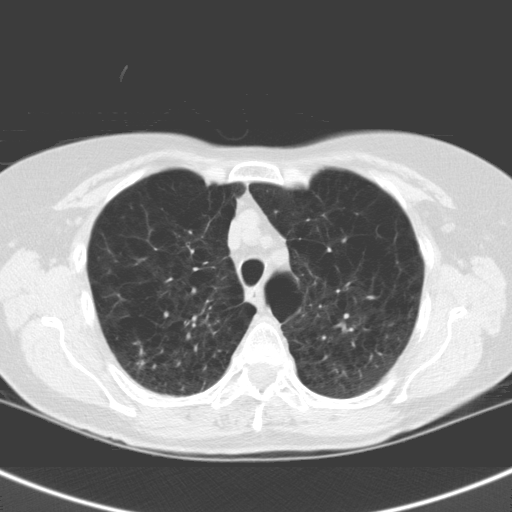
Low-dose screening chest CT, one axial slice; lung window (W 1500 / L -600 HU); 3.2 mm slice thickness; 512 × 512 image matrix, field of view 301 × 301 mm.
Structures marked on this image (manually delineated by an expert):
- lesion 1 (tumor, upper lobe of right lung): bounding box (x1, y1, x2, y2) in pixels: (137, 360, 145, 366)